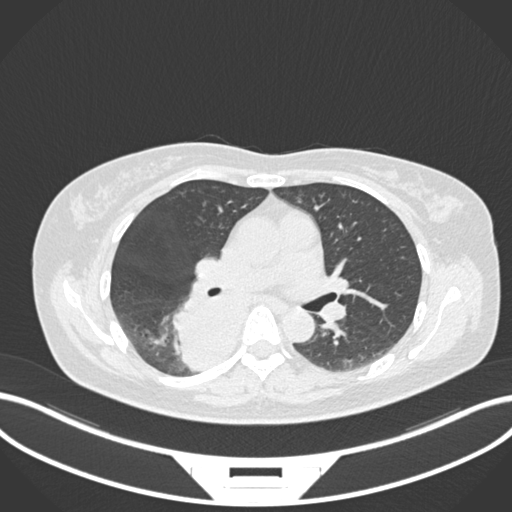
Chest CT, one axial slice. Slice 602 of 677 in the series (ordered by position). Lung window (W 1500 / L -600 HU). 512 × 512 image matrix. Female patient, age 54 years. From the clinical record (not read from this slice): clinical TNM (as recorded): T4 N0 M0.
Structures marked on this image (bounding box drawn by a radiologist):
- lung tumour (recorded histology: adenocarcinoma): bounding box <171,291,254,375> (left, top, right, bottom; pixels)